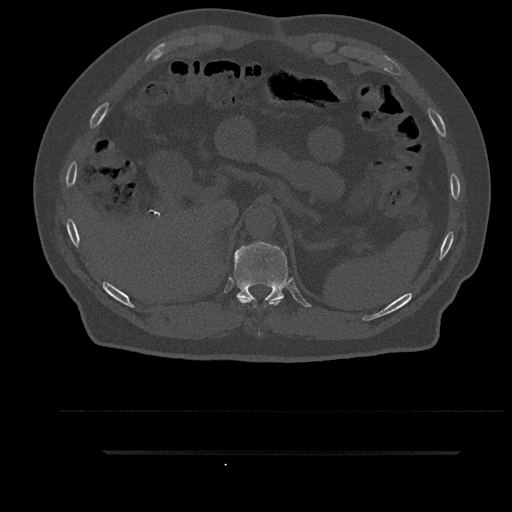
CT including the spine, one axial slice; slice 329 of 797 in the series (ordered by position); reconstruction kernel Br40s/3; 120 kVp; bone window (W 1800 / L 400 HU); 0.5 mm slice thickness; 512 × 512 image matrix, field of view 432 × 432 mm. Male patient, age 63 years. Case-level facts recorded for this patient, not image findings: primary cancer: renal.
Outlined on this slice (semi-automatically segmented with operator editing):
- T10 vertebra: bounding box <238,297,280,336> (left, top, right, bottom; pixels)
- T11 vertebra: <234,241,288,302>